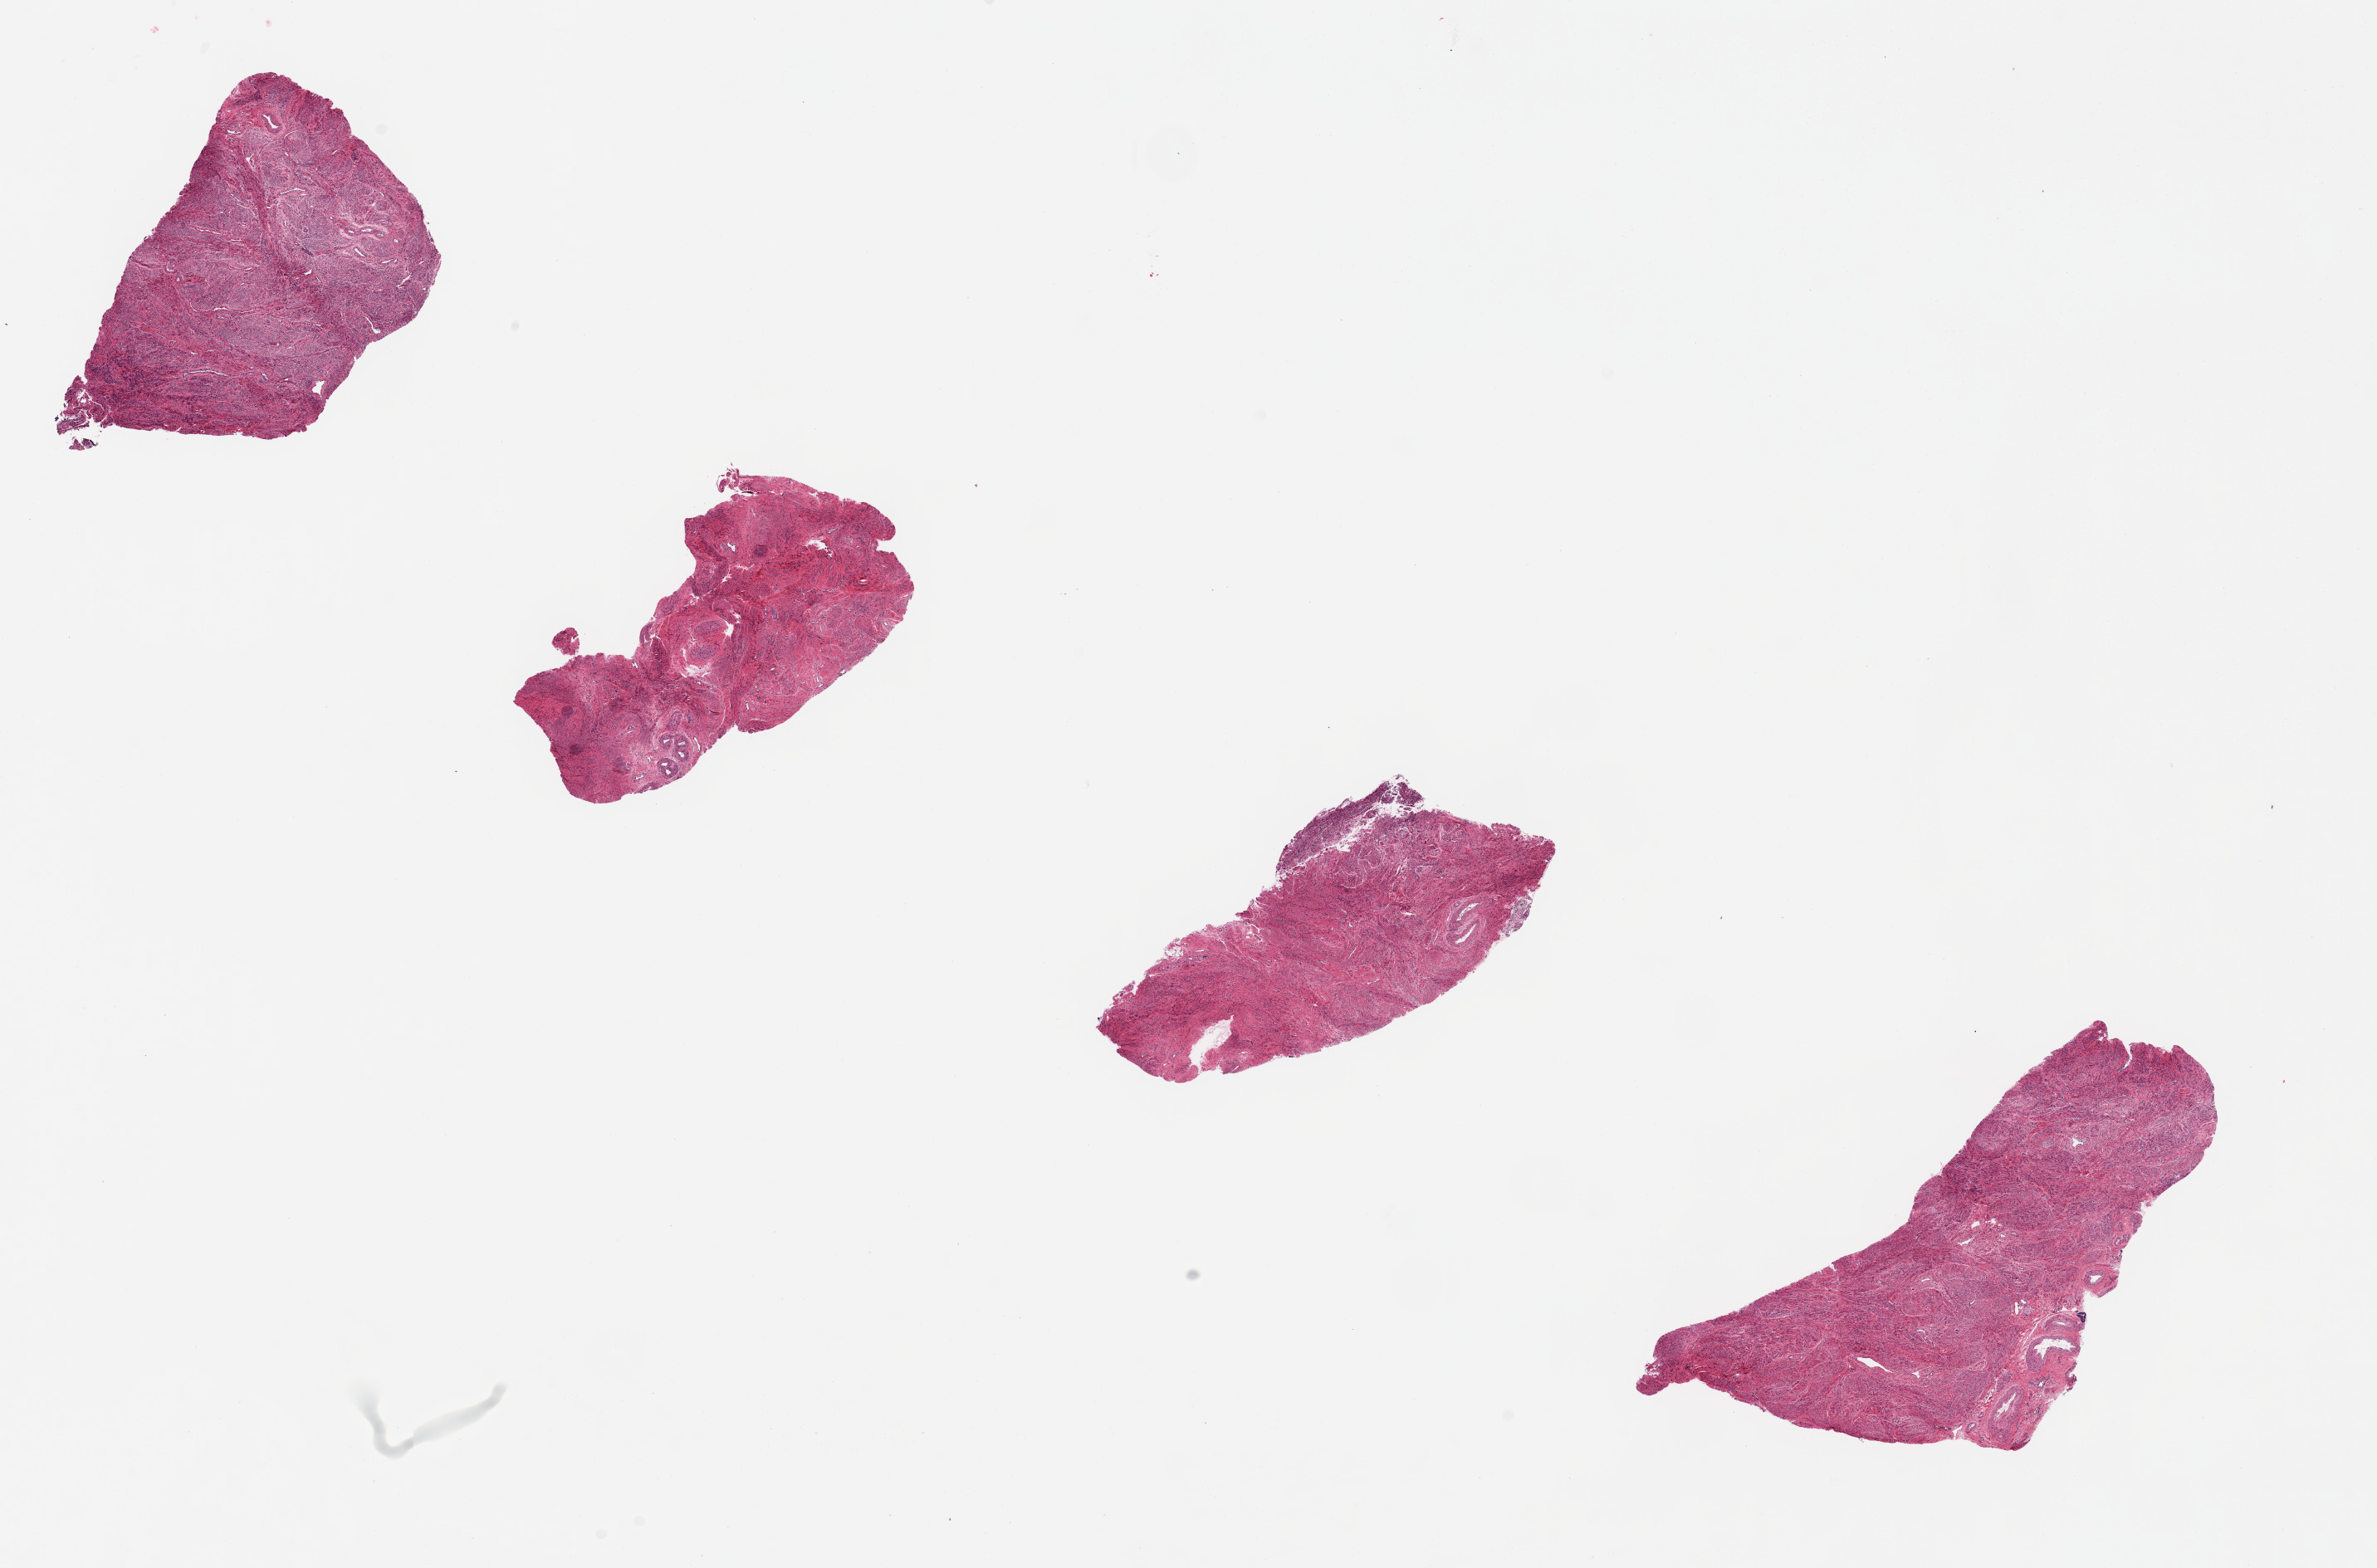
Digitized haematoxylin and eosin-stained section, a low-resolution overview of the entire scanned area, about 22.6 x 14.9 mm. PAXgene-fixed, paraffin-embedded tissue. Section of endocervix (target tissue). Donor tissue sample. Donor sex: female.
Review note (as recorded): 4 ~5x2.5 mm pieces of fibromuscular stroma and one gland.